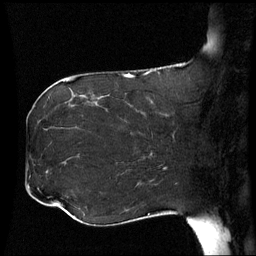
Breast MRI (dynamic contrast-enhanced), one sagittal slice; position 24 of 60 along the scan axis; dynamic contrast-enhanced series, image 2 of 3 at this slice position (ordered by acquisition); 1.5 T; TE 4.2 ms, TR 8.9 ms; 2.5 mm slice thickness; 256 × 256 image matrix, field of view 230 × 230 mm. Patient: female, 42 years. From the clinical record (not read from this slice): setting: breast cancer imaged before/during neoadjuvant chemotherapy; receptor status: HER2-positive.
Outlined on this slice (semi-automatically segmented with operator editing):
- analysis volume of interest (the breast-tissue region the enhancement analysis was run in; not a lesion): bounding box <106,102,173,150> (left, top, right, bottom; pixels)
- tumour enhancement mask (voxels above the 70 % enhancement threshold inside the analysis volume of interest): <141,113,167,117>